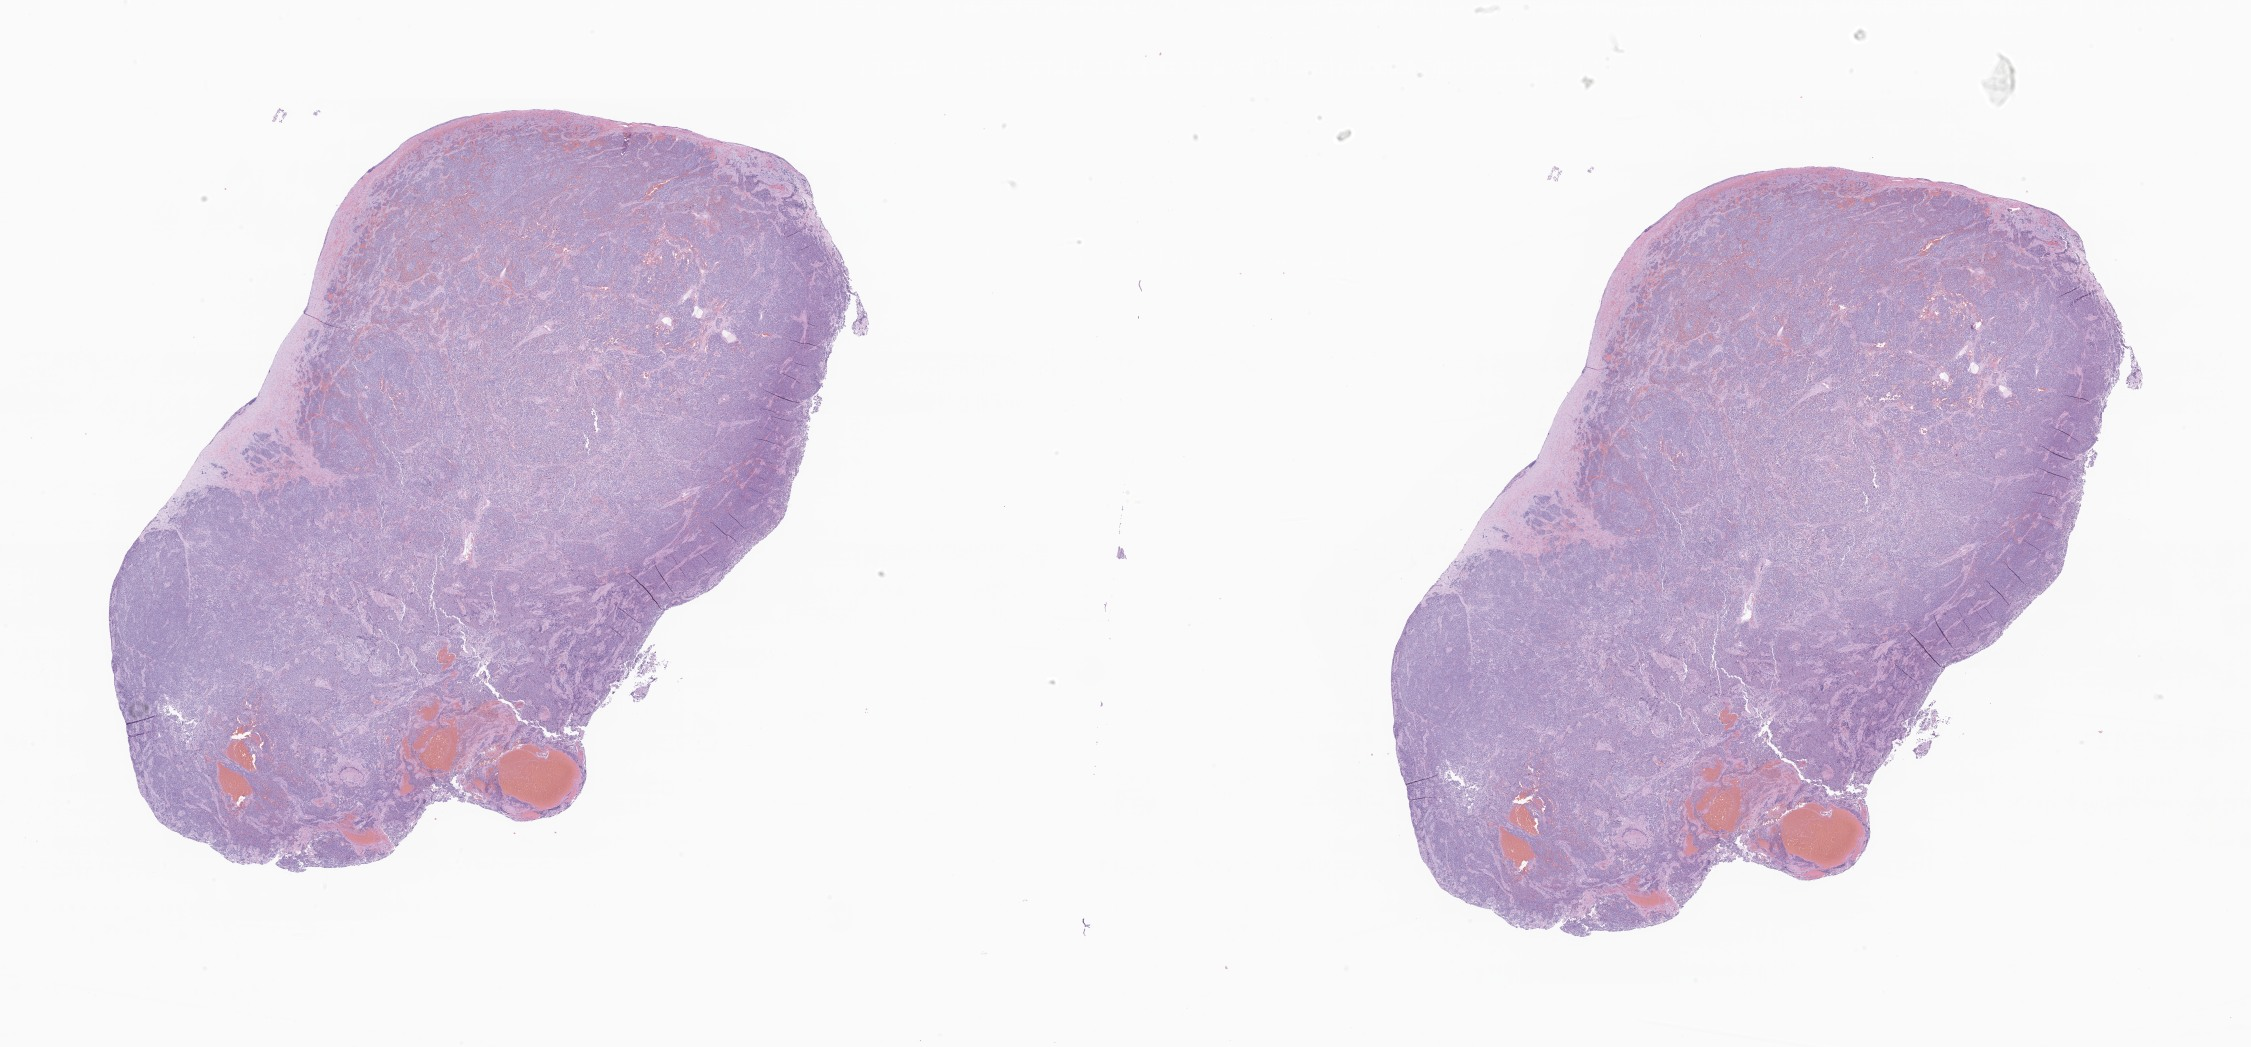
Digitized H&E-stained section of tumor tissue from the retroperitoneum, shown as a low-resolution overview of the whole scanned area (about 38.0 x 17.7 mm); formalin-fixed paraffin-embedded section. Female patient, age 644 days (about 1.8 years).
Diagnosis: Neuroblastoma, NOS.